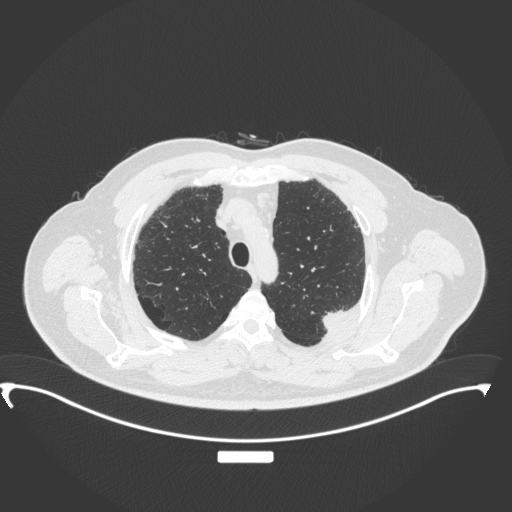
Chest CT, one axial slice; position 287 of 350 along the scan axis; lung window (W 1500 / L -600 HU); 1 mm slice thickness; 512 × 512 image matrix, field of view 459 × 459 mm. Male patient, age 64 years. Case-level facts recorded for this patient, not image findings: clinical TNM (as recorded): T1c N1 M1.
Outlined on this slice (rectangle marked by the reading radiologist):
- lung tumour (recorded histology: adenocarcinoma): bounding box [x1, y1, x2, y2] px = [318, 305, 355, 334]